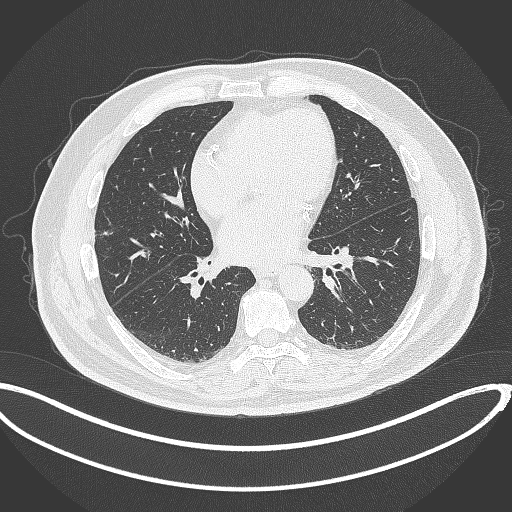
Chest CT, one axial slice. Position 146 of 340 along the scan axis. 120 kVp. Lung window (W 1500 / L -600 HU). 1 mm slice thickness. 512 × 512 image matrix. Male patient, age 68 years. From the clinical record (not read from this slice): clinical TNM (as recorded): T1c N0 M0.
Outlined on this slice (bounding box drawn by a radiologist):
- lung tumour (recorded histology: adenocarcinoma): bounding box <100,226,115,240> (left, top, right, bottom; pixels)